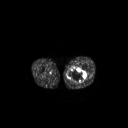
FDG PET of an extremity soft-tissue mass (from a PET/CT study), one axial slice; position 237 of 267 along the scan axis; 3.27 mm slice thickness; 128 × 128 image matrix. Patient: male, 44 years. From the clinical record (not read from this slice): histological type: undifferentiated pleomorphic liposarcoma; grade: high; site of the primary tumour: left thigh.
Annotated regions visible in this slice (expert contour drawn on MRI and transferred to this co-registered scan by the dataset authors):
- gross tumour volume including surrounding oedema: bounding box (x1, y1, x2, y2) in pixels: (67, 68, 86, 83)
- gross tumour volume (mass): (67, 68, 86, 83)